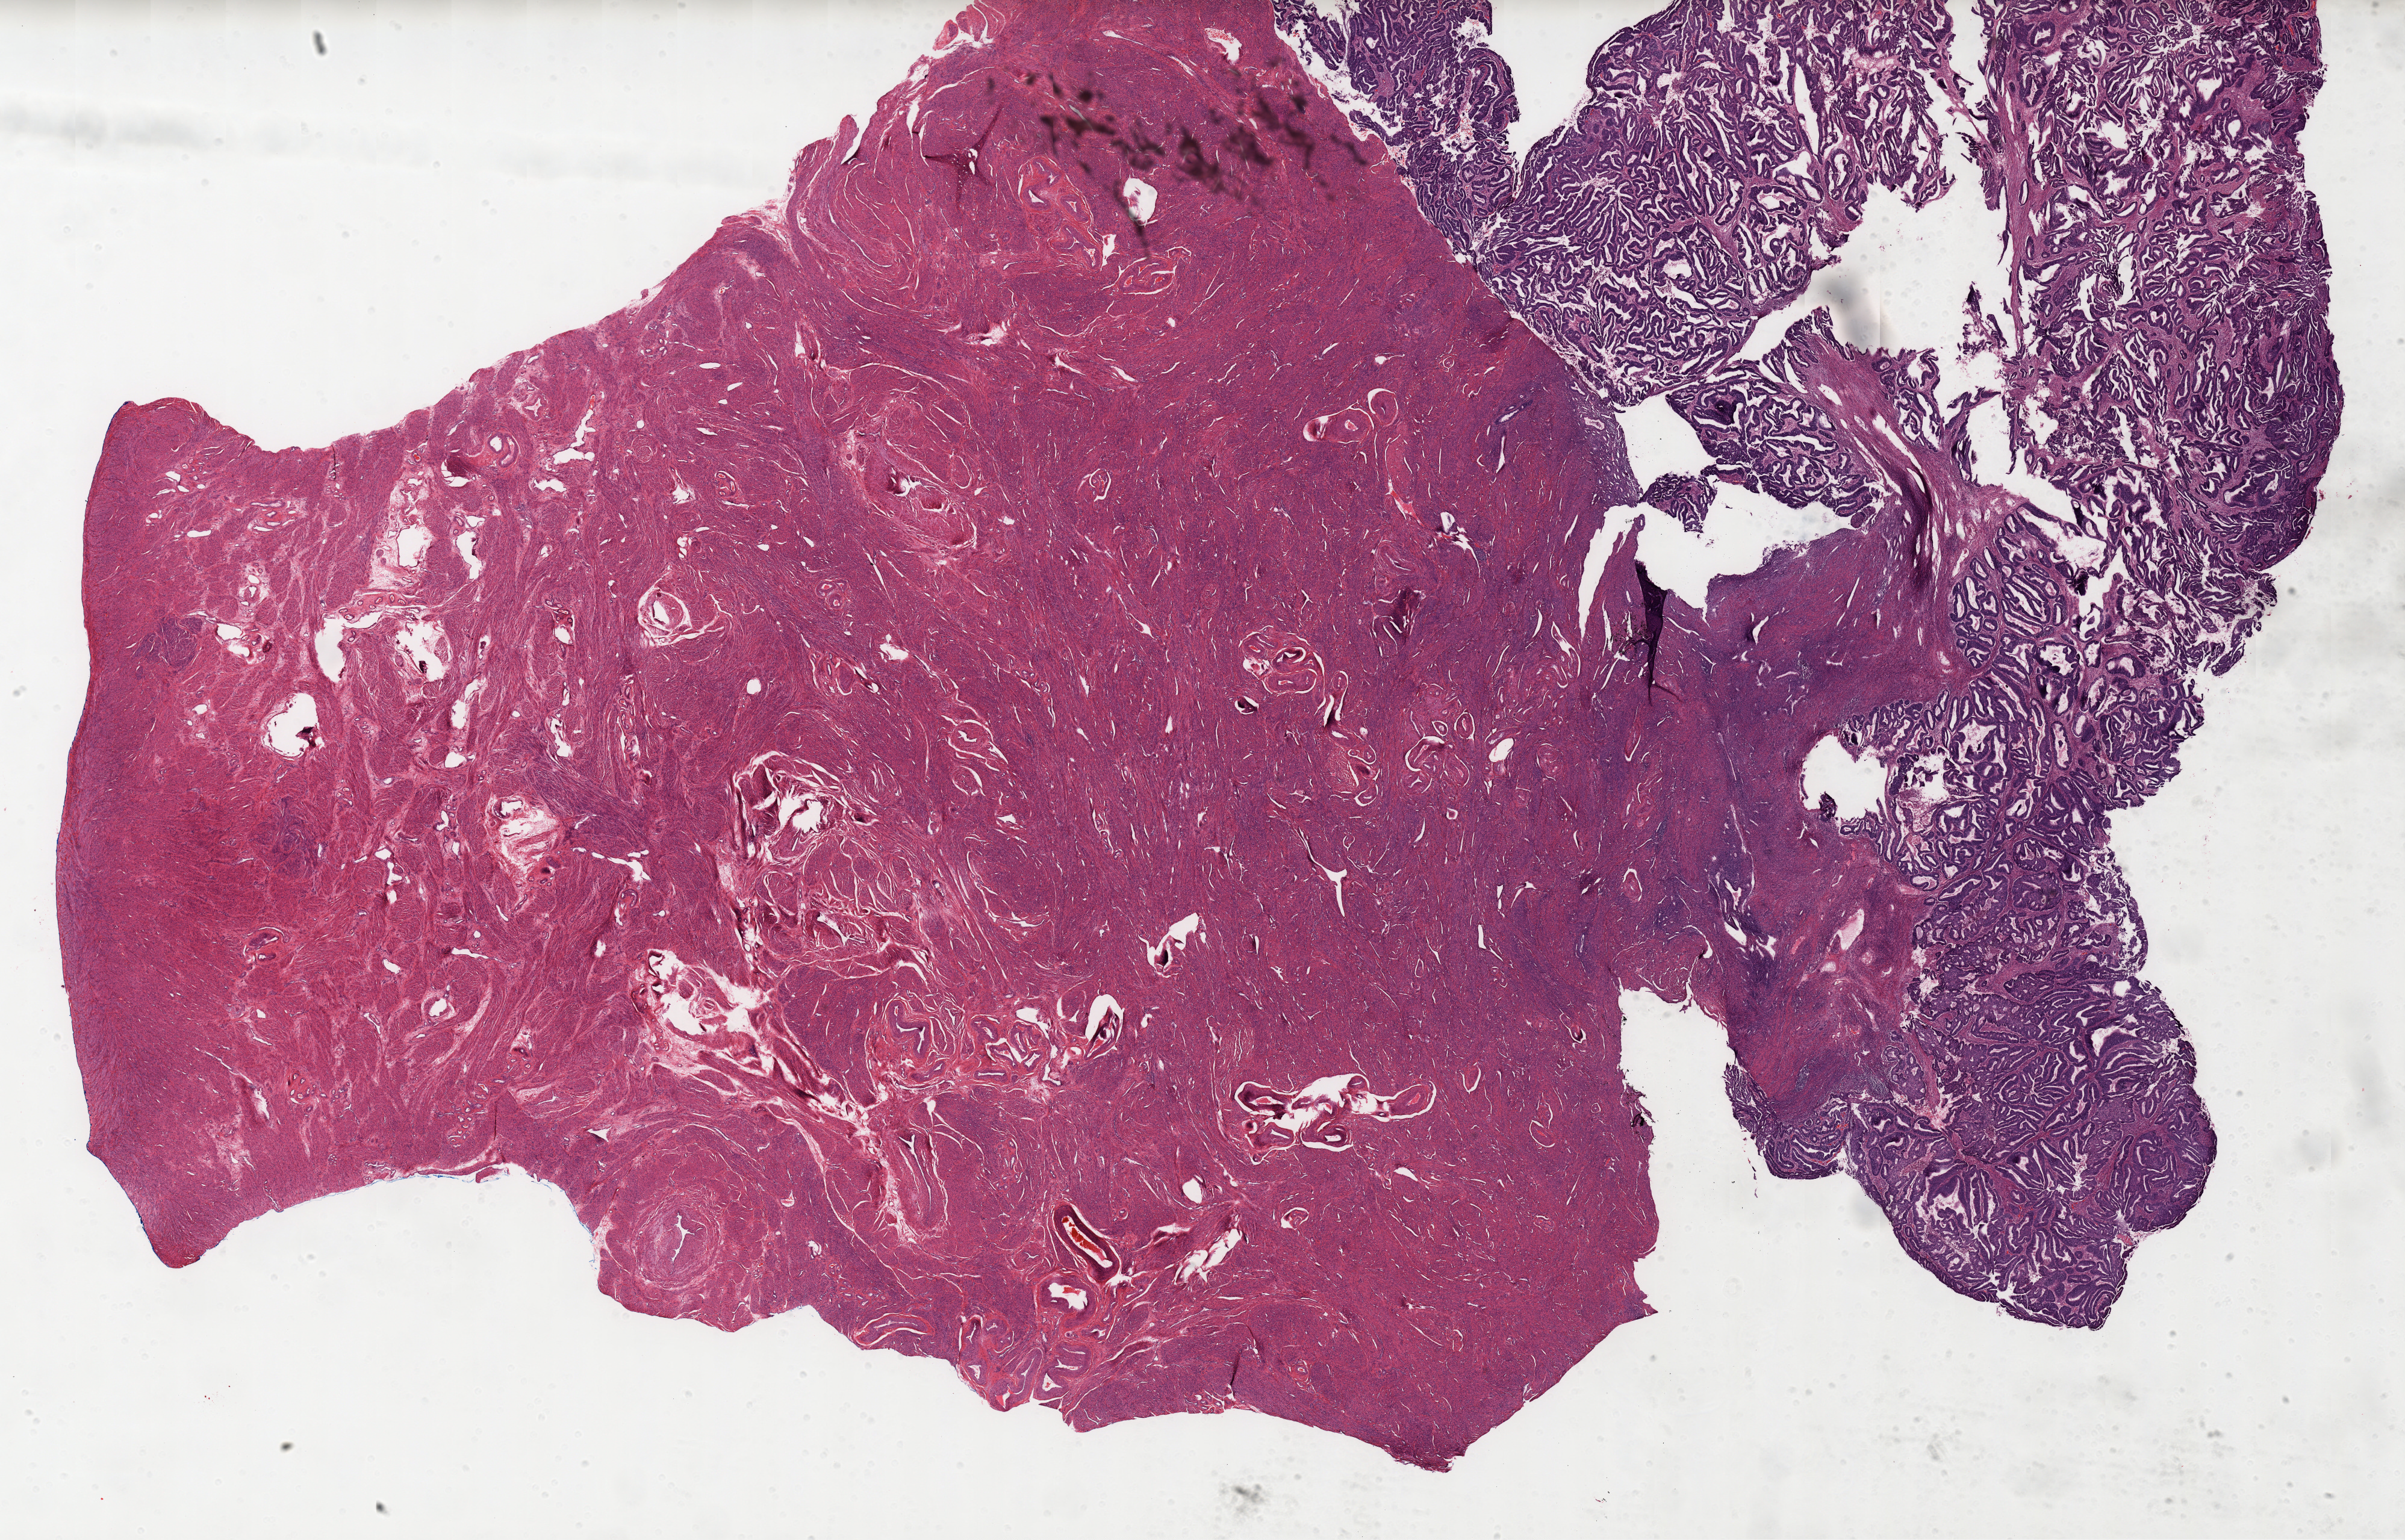
Whole-slide histology image, Hematoxylin and eosin (H&E) stained — whole scanned area (about 31.8 x 20.4 mm, slide scanned at 20x) shown as a low-resolution overview, formalin-fixed paraffin-embedded (FFPE) diagnostic section, primary tumour sample from the uterus. Patient: female, age at initial diagnosis 57 years. Histologic grade: G3 (poorly differentiated).
- diagnosis: Endometrioid adenocarcinoma, NOS (endometrium)
- FIGO stage: IA